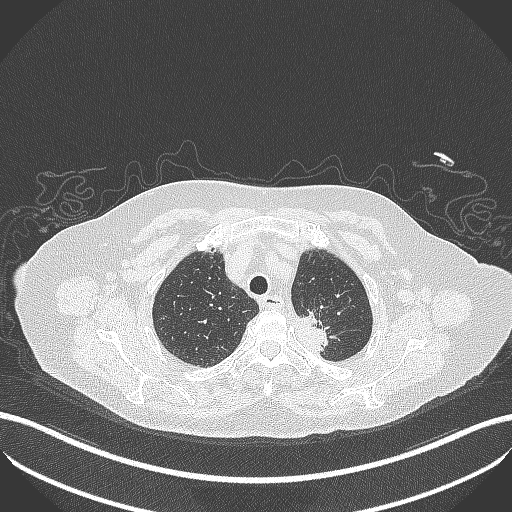
Chest CT, one axial slice; slice 284 of 353 in the series (ordered by position); lung window (W 1500 / L -600 HU); 1 mm slice thickness; 512 × 512 image matrix, field of view 400 × 400 mm. Female patient, age 81 years. From the clinical record (not read from this slice): clinical TNM (as recorded): T2a N0 M0.
Annotated regions visible in this slice (bounding box drawn by a radiologist):
- lung tumour (recorded histology: adenocarcinoma): bounding box (x1, y1, x2, y2) in pixels: (287, 304, 332, 360)